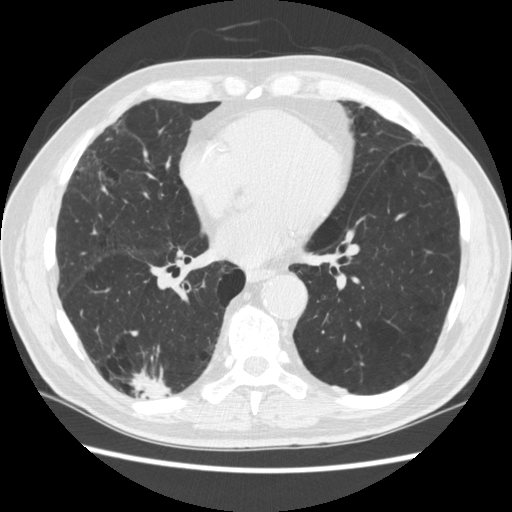
Low-dose screening chest CT, one axial slice. Position 117 of 266 along the scan axis. Reconstruction kernel STANDARD. 120 kVp. Lung window (W 1500 / L -600 HU). 1.25 mm slice thickness. 512 × 512 image matrix.
Outlined on this slice (expert manual segmentation):
- lesion 1 (tumor, upper lobe of right lung): box from (x=132, y=373) to (x=170, y=399) px